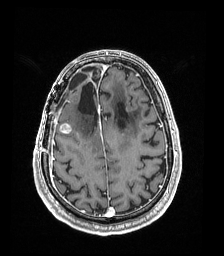
Brain MRI from a brain-tumour surgery series, one axial slice. Position 53 of 192 along the scan axis. T1-weighted post-contrast. 1 mm slice thickness. 224 × 256 image matrix, field of view 224 × 256 mm. Case-level facts recorded for this patient, not image findings: histopathology: Astrocytoma; WHO grade: 4; IDH mutation: yes.
Outlined on this slice (outlined manually by an expert reader):
- previous resection cavity: box from (x=78, y=70) to (x=98, y=123) px